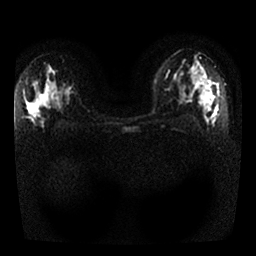
Breast MRI, one axial slice. Position 15 of 25 along the scan axis. Diffusion-weighted series; image 2 of 4 stored at this slice position (different b-values; order by instance number). 1.5 T. 4 mm slice thickness. 256 × 256 image matrix, field of view 320 × 320 mm. Female patient.
Structures marked on this image (manually delineated by an expert):
- tumour on diffusion-weighted imaging: bounding box <196,84,213,95> (left, top, right, bottom; pixels)